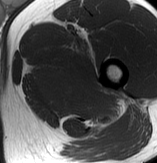
MRI of an extremity soft-tissue mass, one axial slice. Slice 63 of 70 in the series (ordered by position). MR volume resampled by the dataset authors to the PET/CT grid (not the native acquisition matrix). 3.27 mm slice thickness. 157 × 163 image matrix, field of view 153 × 159 mm. Male patient. Case-level facts recorded for this patient, not image findings: histological type: extraskeletal osteosarcoma; grade: high; site of the primary tumour: left adductur.
Structures marked on this image (expert contour drawn on MRI and transferred to this co-registered scan by the dataset authors):
- gross tumour volume (mass): box from (x=31, y=34) to (x=125, y=125) px